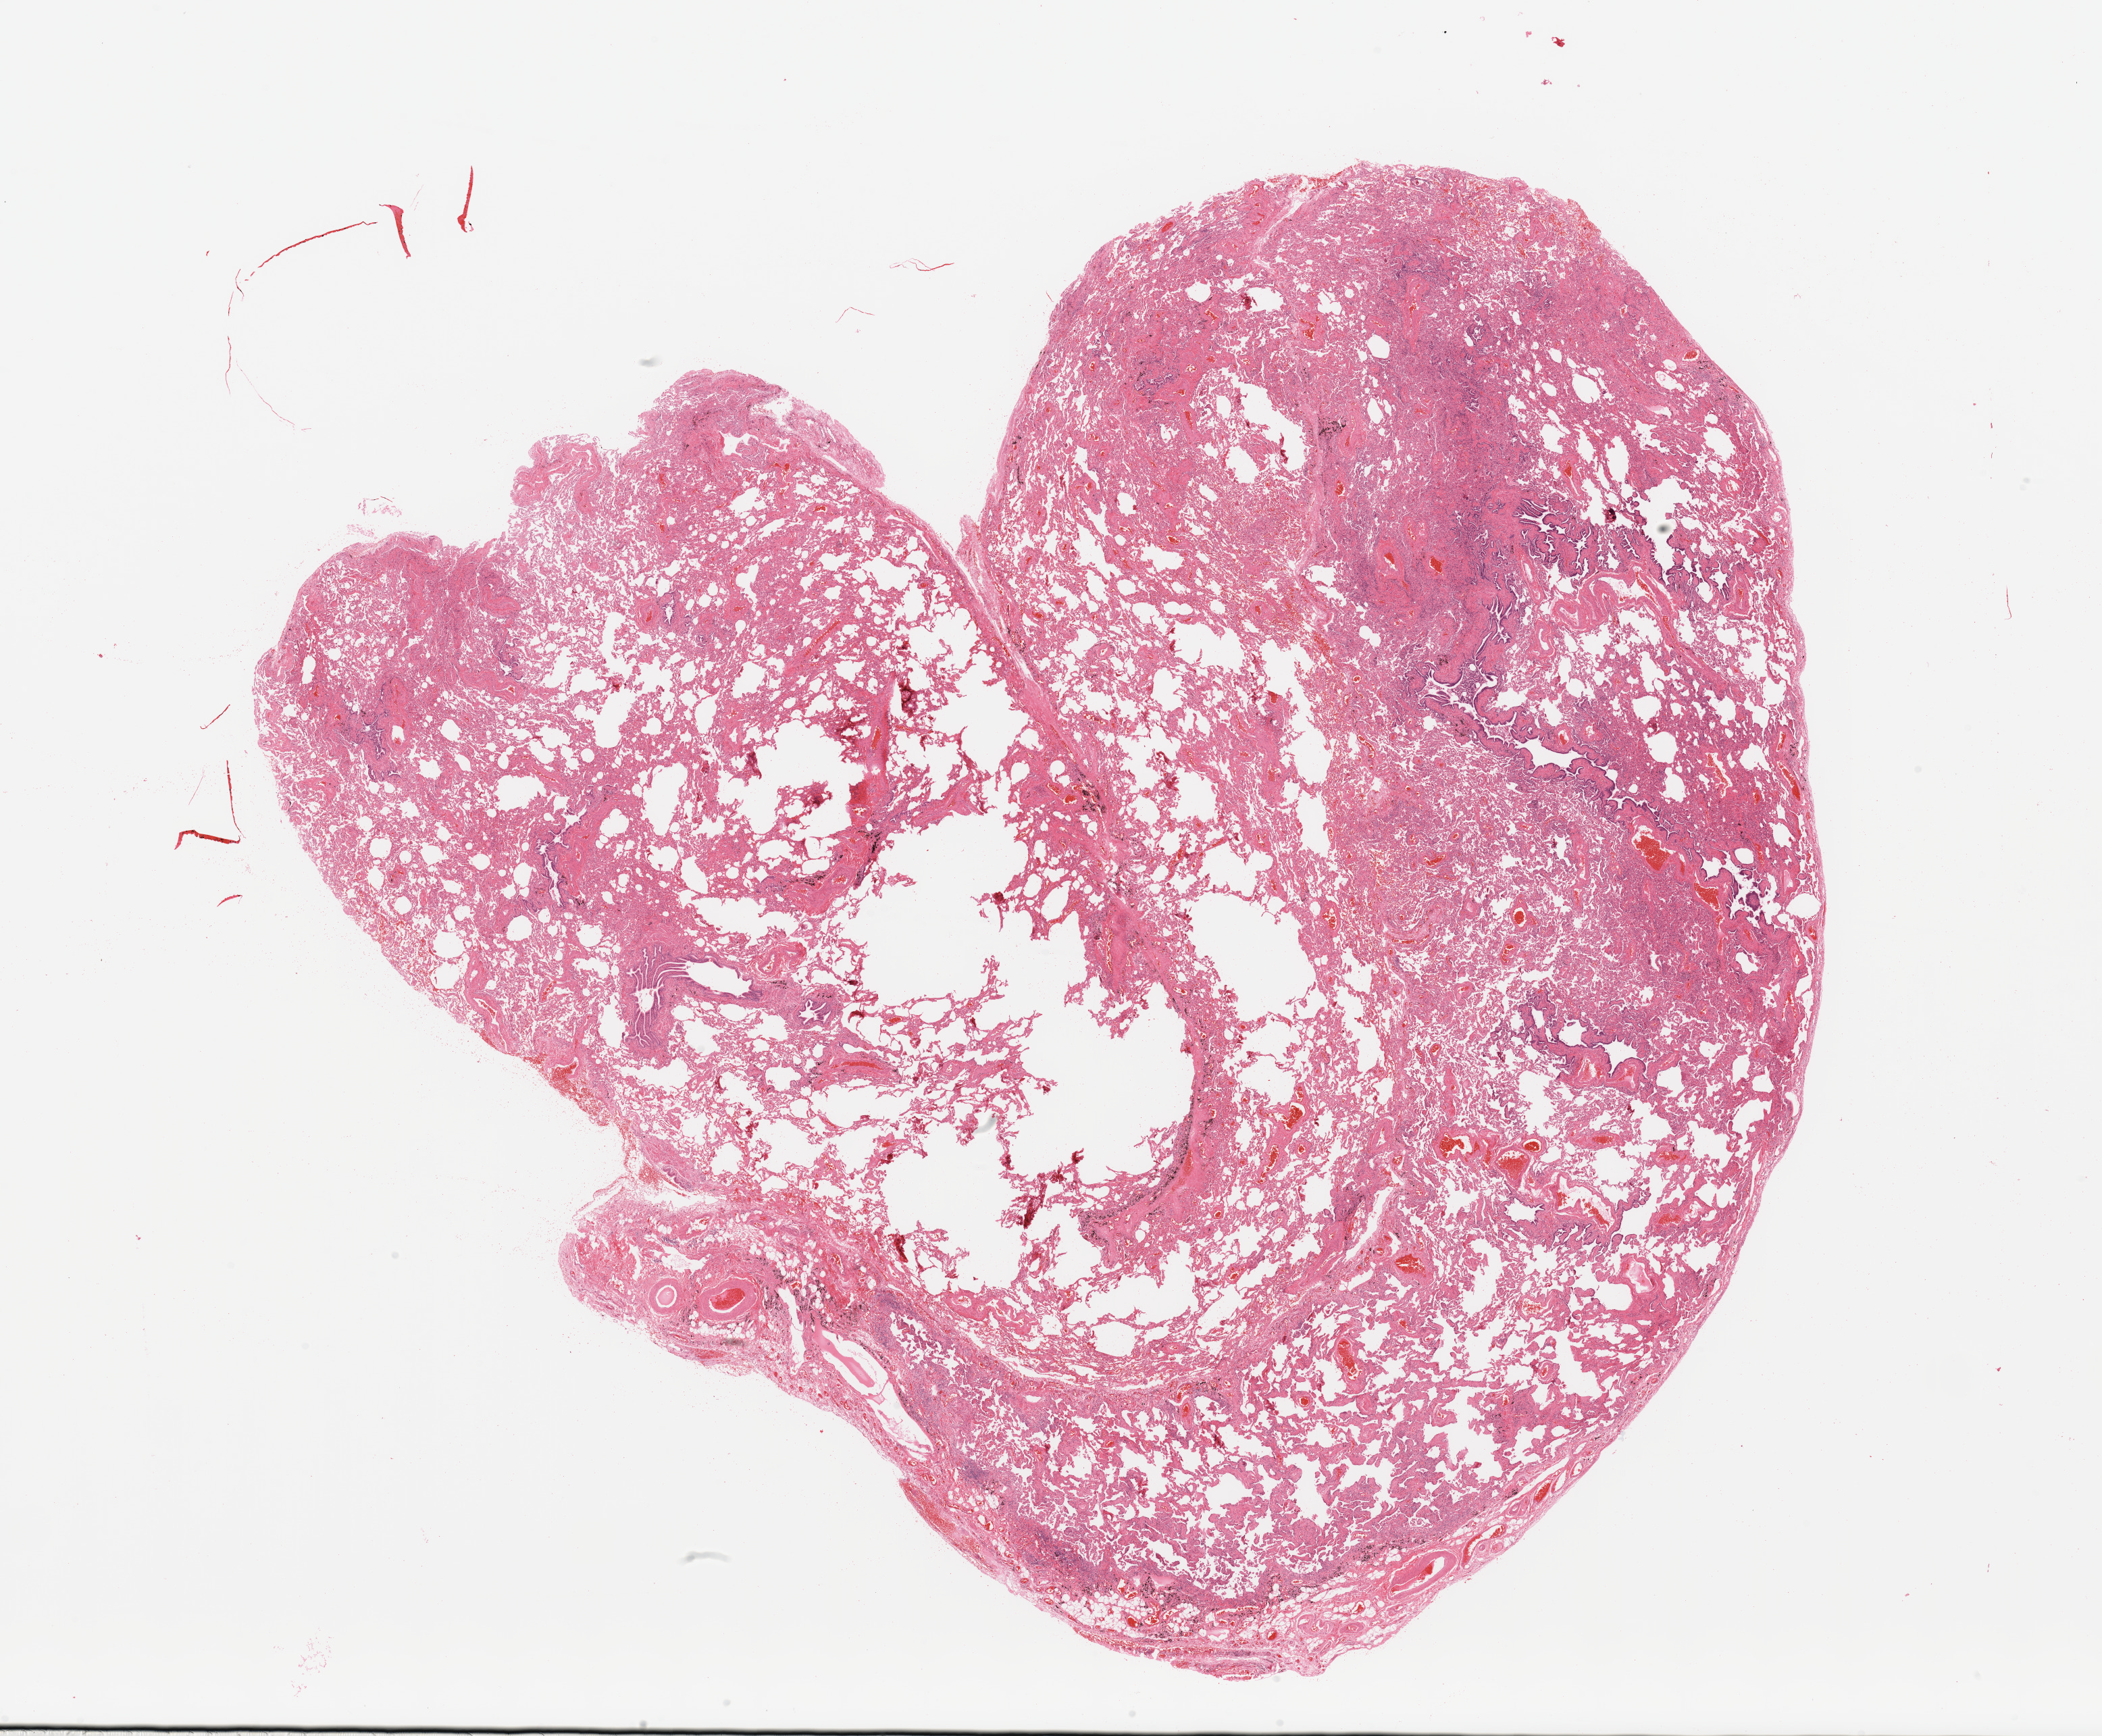
Digitized Hematoxylin and eosin (H&E) stained tissue section (whole slide) — a low-resolution overview of the entire scanned area, about 24.6 x 20.3 mm (slide scanned at 20x), lung, tissue type not recorded.
• patient diagnosis (cohort enrolment): lung adenocarcinoma (lung)